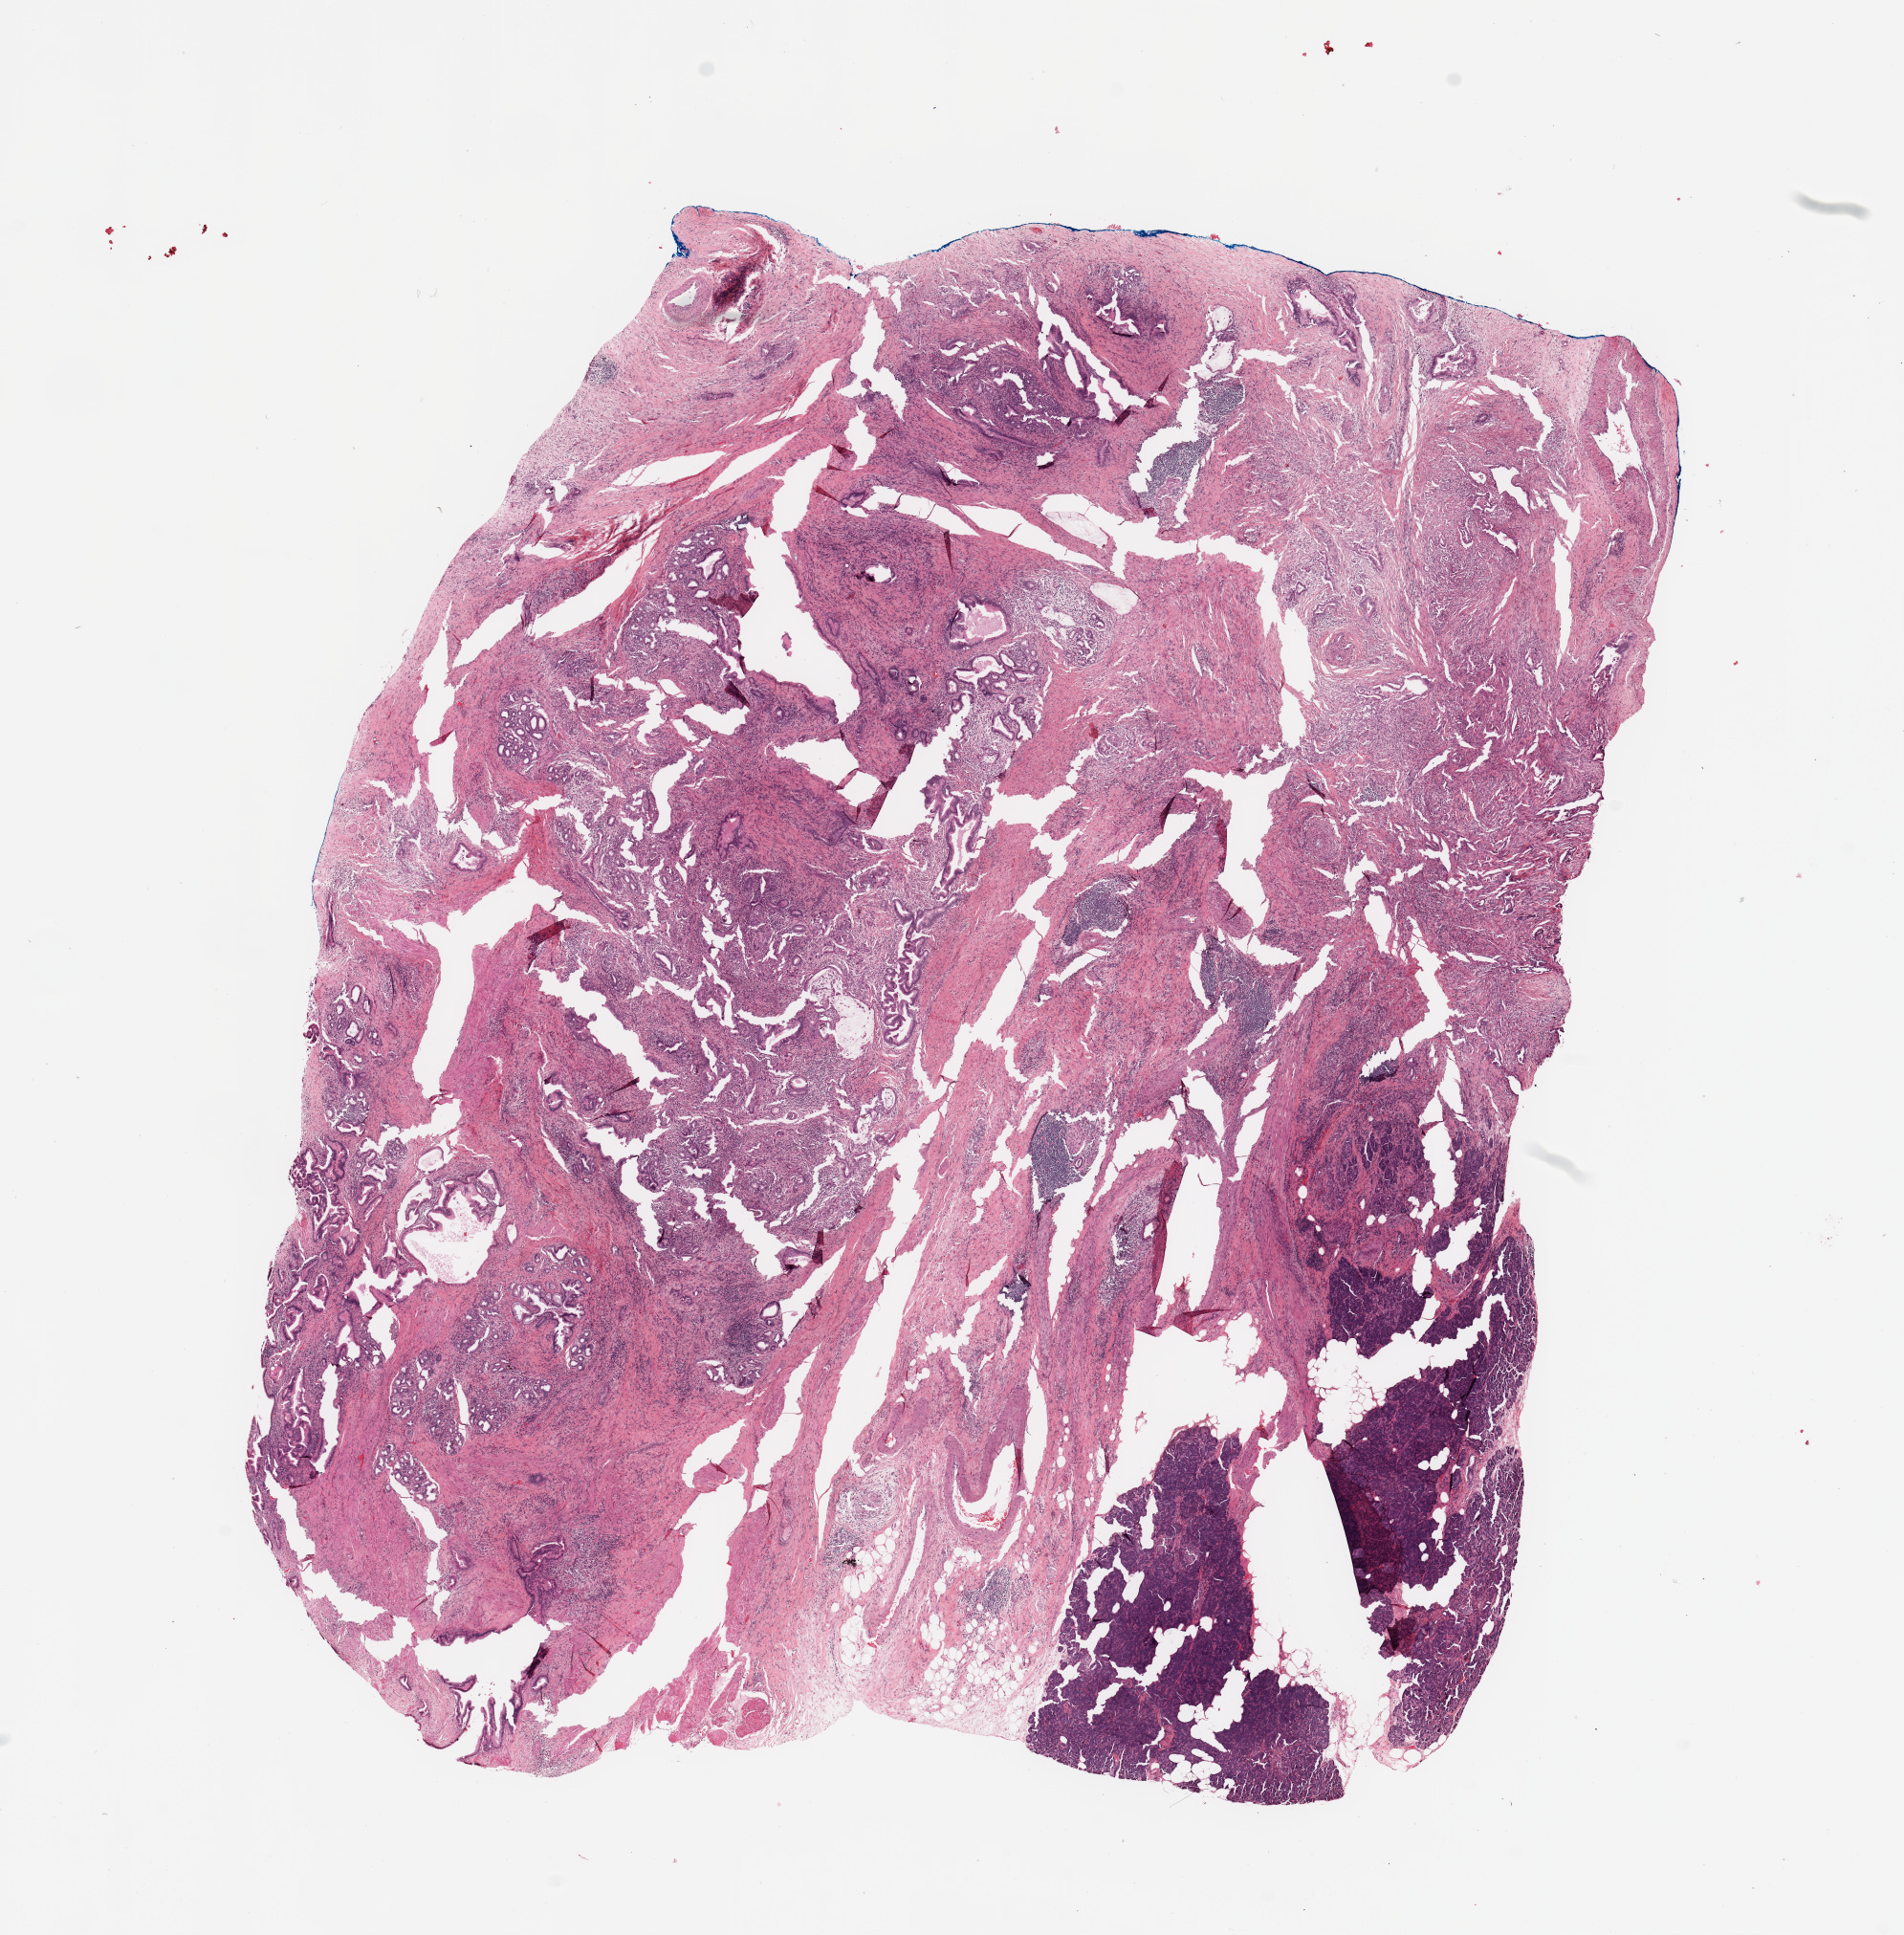
Whole-slide histology image, H&E — shown as a low-resolution overview of the whole scanned area (about 15.8 x 16.0 mm). Pancreas, tumour tissue. Patient: female, age 70 years. Histologic grade: G2 (moderately differentiated).
* AJCC pathologic stage: IIIB
* primary tumour site (as recorded): head
* histologic diagnosis: Infiltrating duct carcinoma, NOS